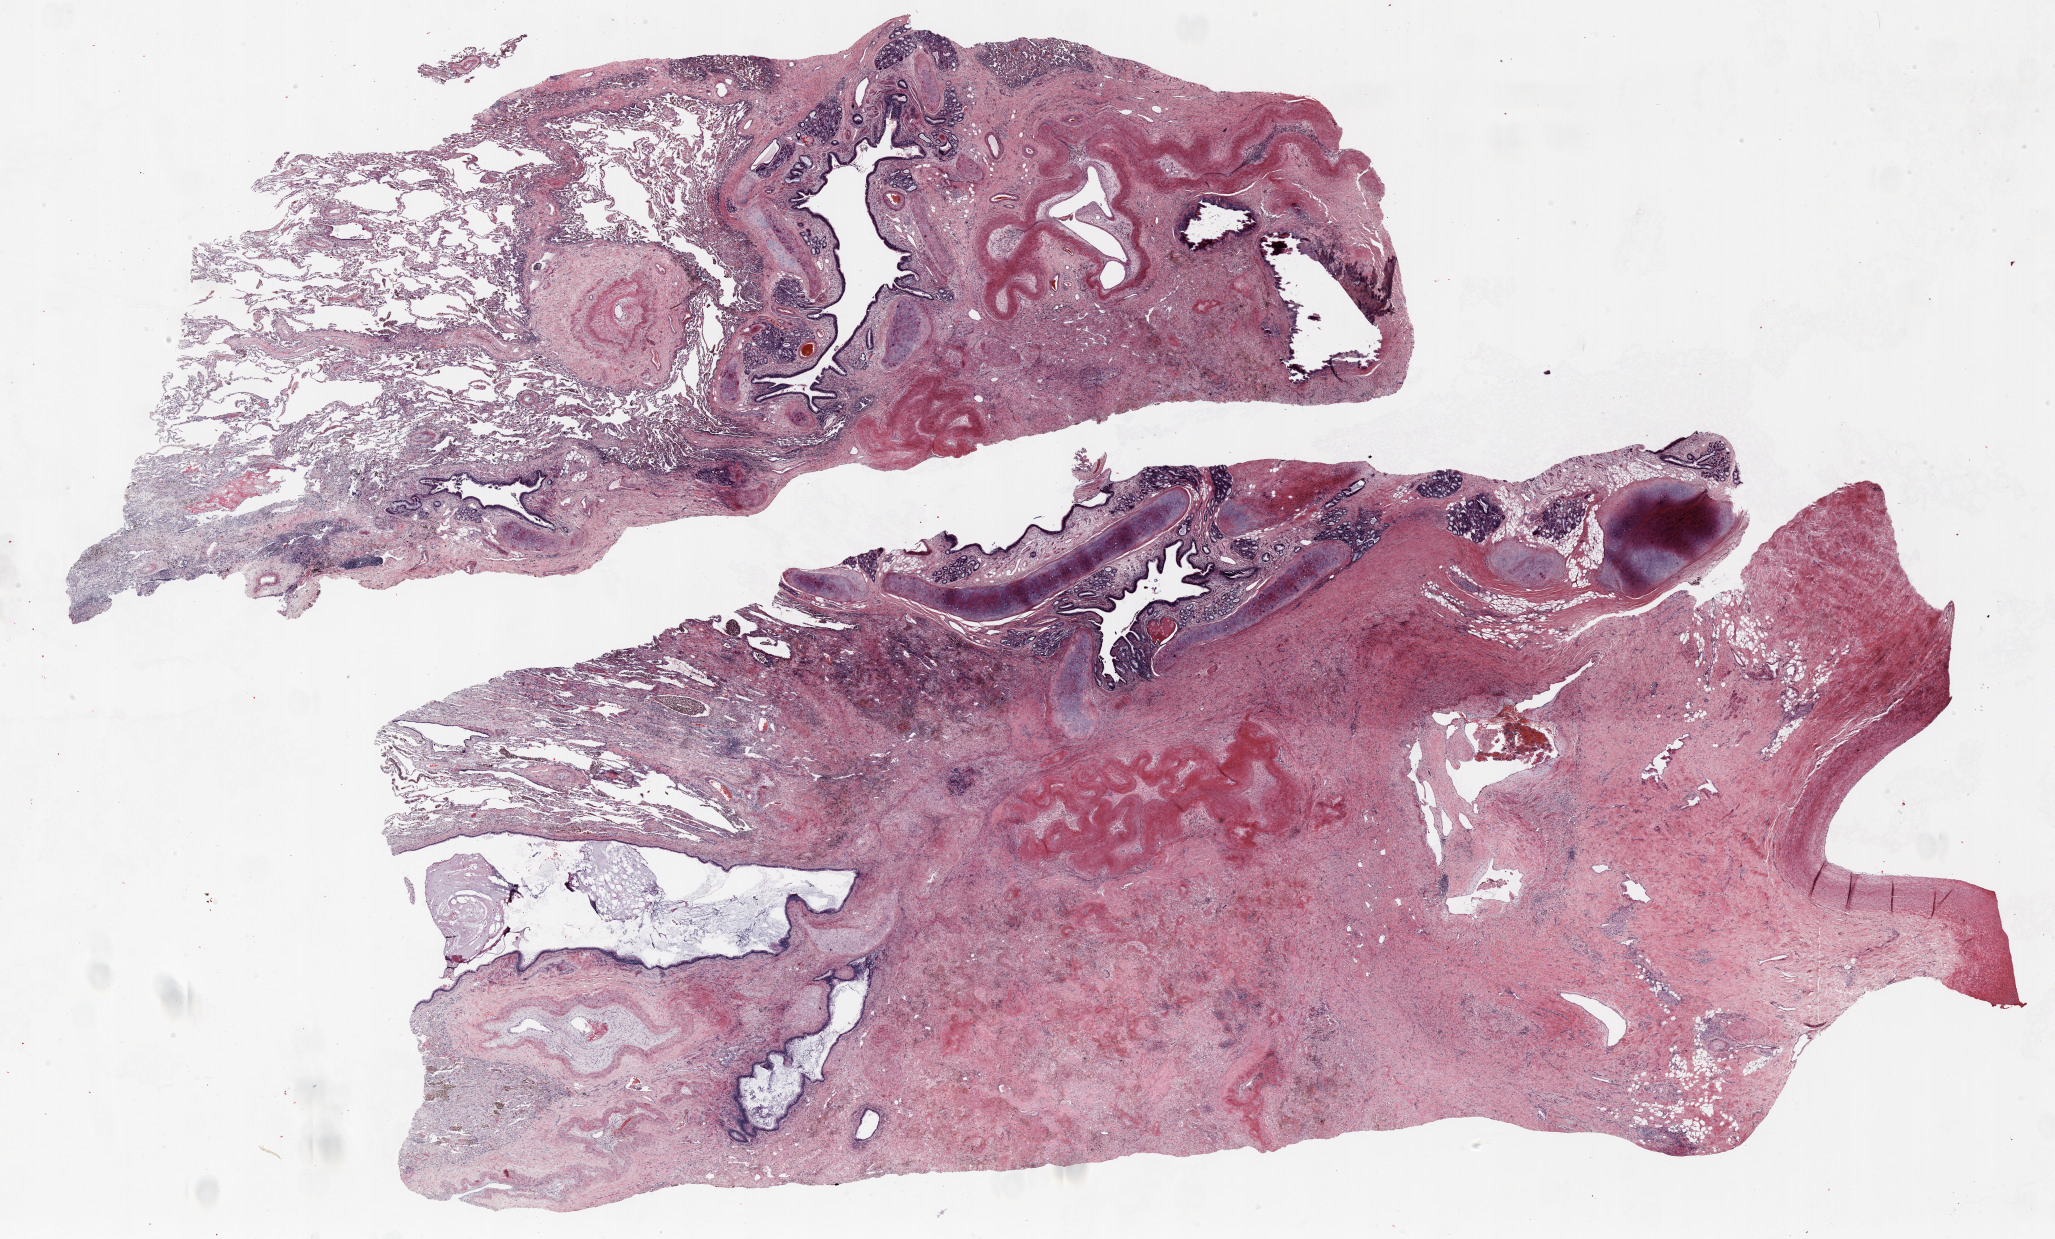
Hematoxylin and eosin (H&E) stained whole-slide image, shown as a low-resolution overview of the whole scanned area (about 33.0 x 19.9 mm), formalin-fixed paraffin-embedded (FFPE) section, lung. Male patient, aged 58 at enrolment. Current smoker at enrolment.
Primary tumour location (clinical record): right upper lobe, right hilum. Tumour size (pathology): 58 mm. Stage (AJCC 6th edition): IB. Participant's lung-cancer diagnosis: Non-small cell carcinoma.